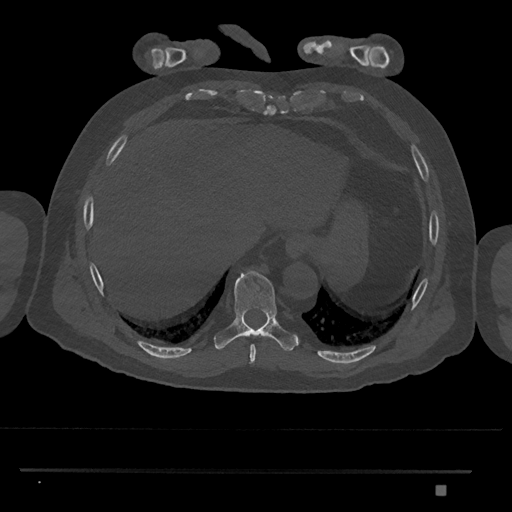
CT including the spine, one axial slice. Slice 1063 of 1134 in the series (ordered by position). Reconstruction kernel Br40s/3. Bone window (W 1800 / L 400 HU). 512 × 512 image matrix. Male patient, age 65 years. Case-level facts recorded for this patient, not image findings: primary cancer: prostate.
Structures marked on this image (semi-automatically segmented with operator editing):
- T8 vertebra: bounding box <249,344,256,365> (left, top, right, bottom; pixels)
- T9 vertebra: <213,270,301,352>